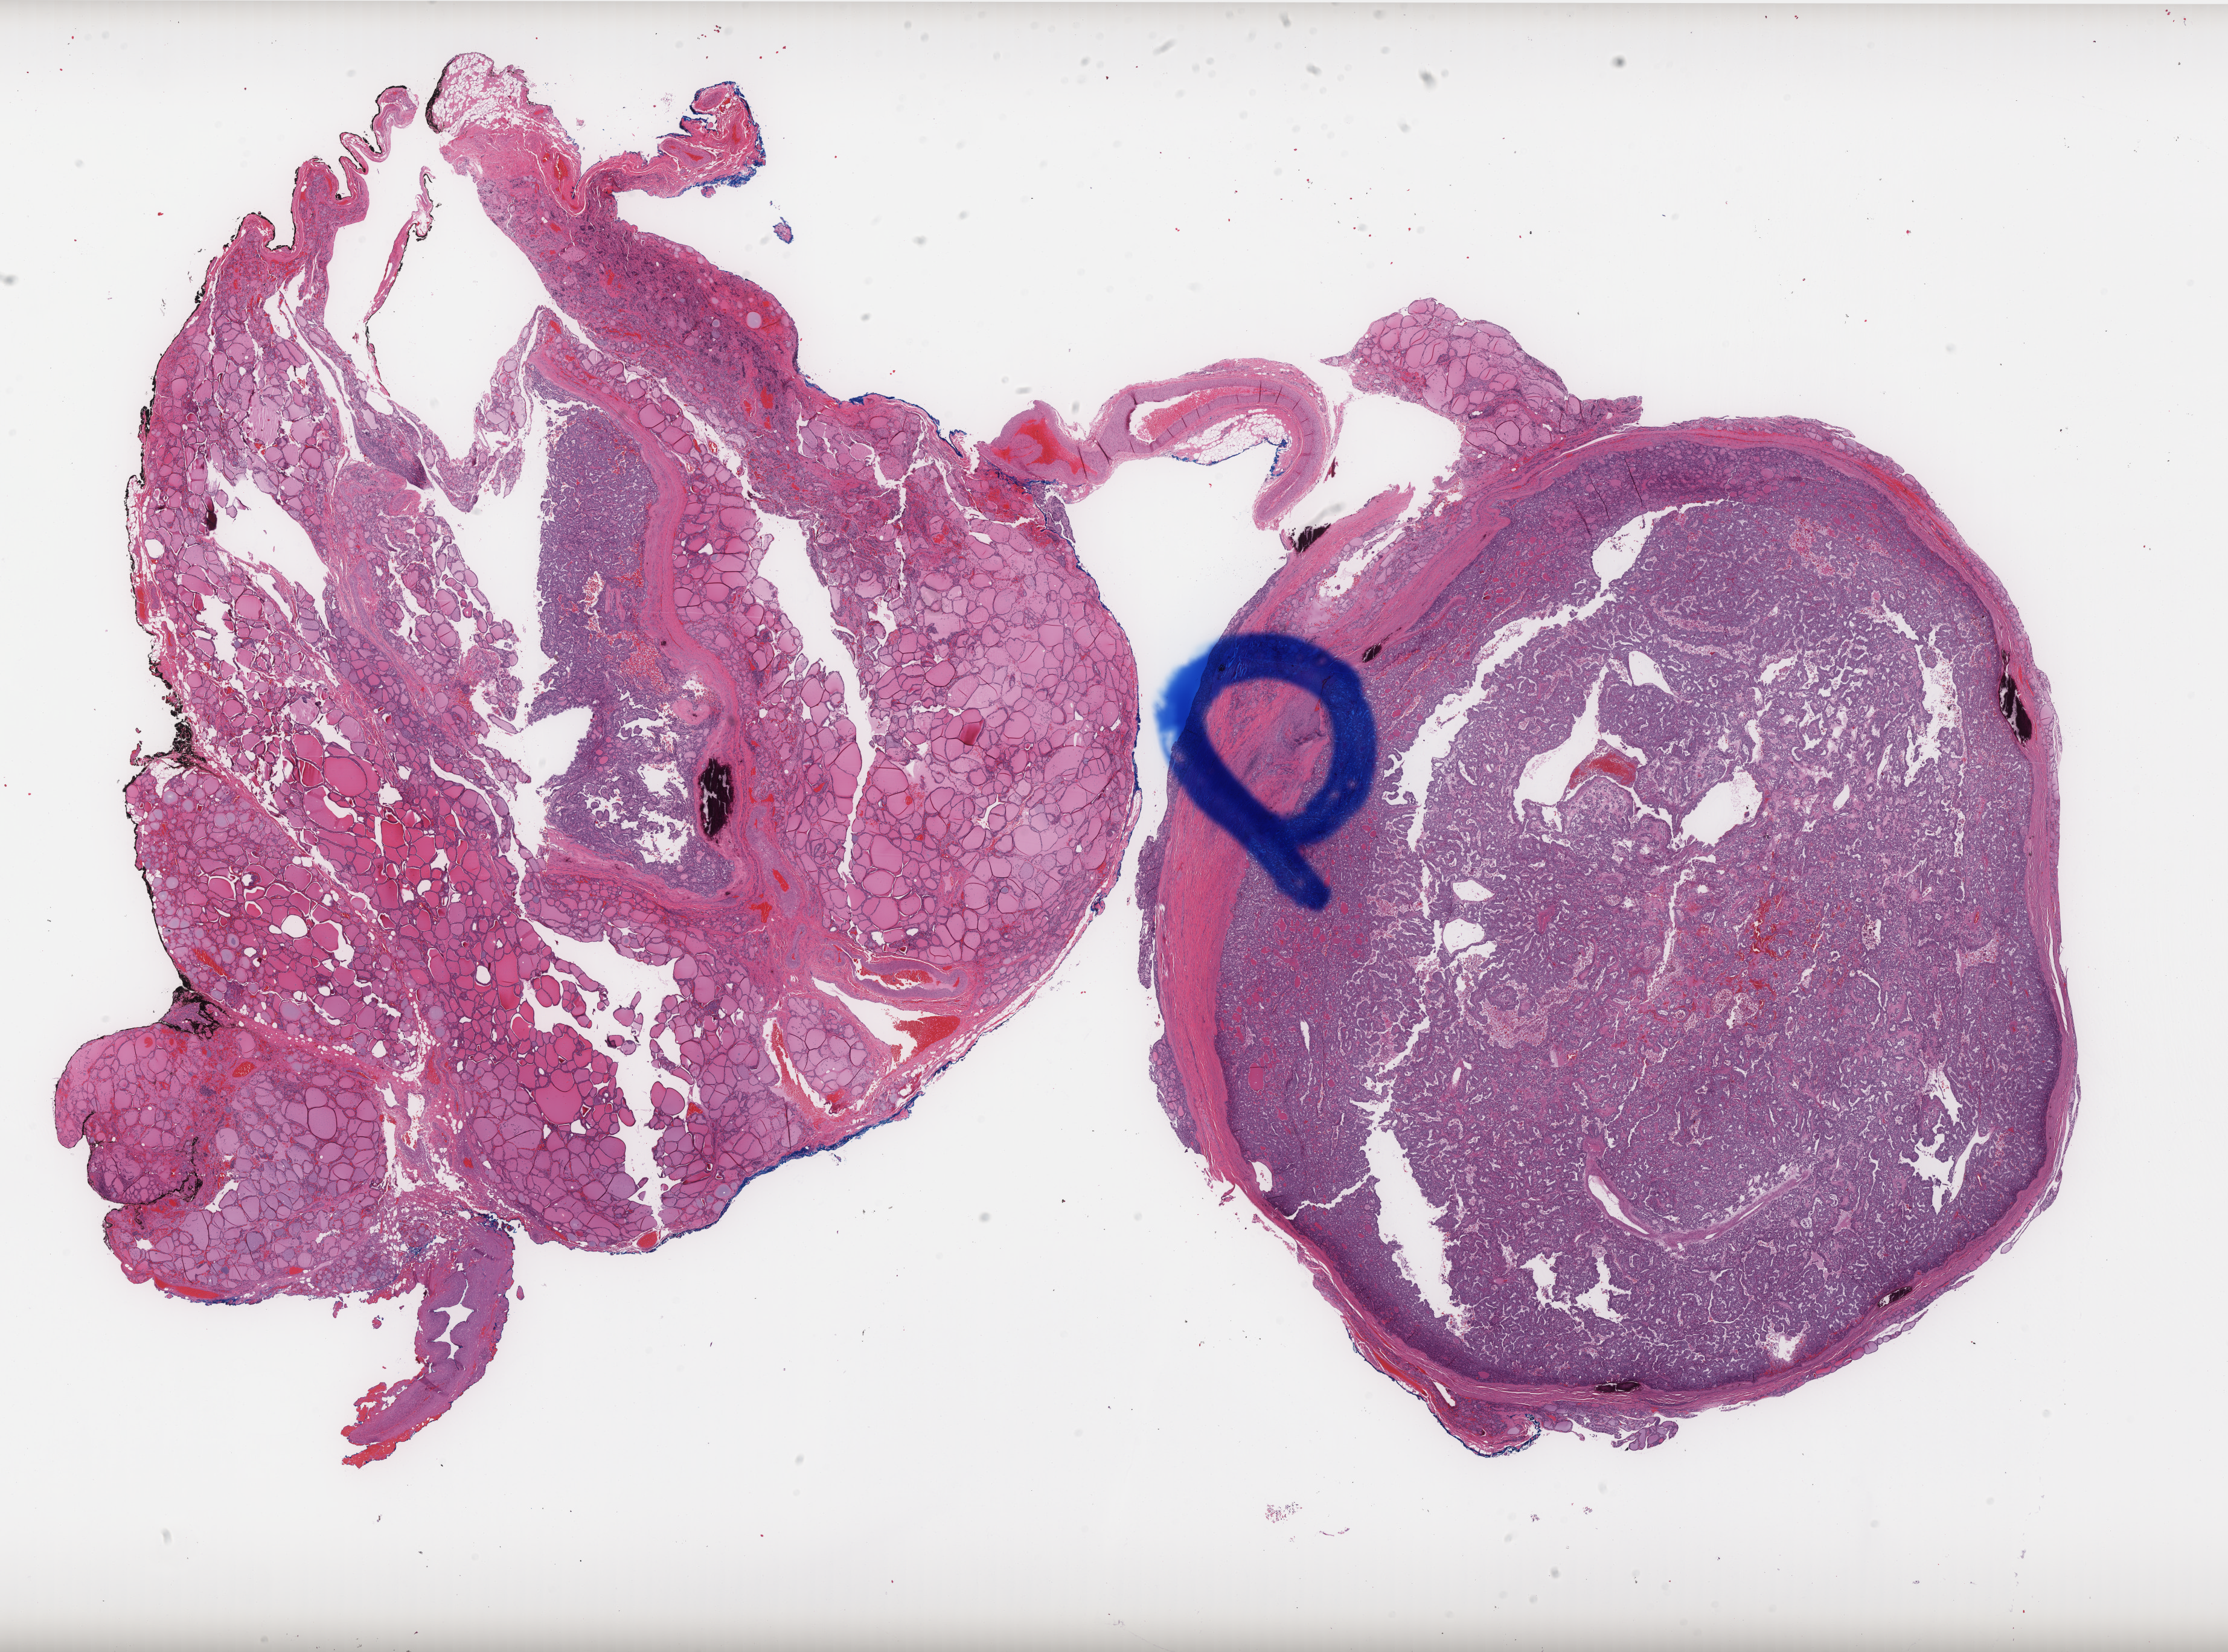
H&E-stained whole-slide image, whole scanned area (about 29.6 x 21.9 mm, slide scanned at 40x) shown as a low-resolution overview; formalin-fixed paraffin-embedded (FFPE) diagnostic section; thyroid, primary tumour sample. Female, age 42 years at initial diagnosis.
Histologic diagnosis: Papillary adenocarcinoma, NOS (thyroid gland). TNM: T1b N0 M0. AJCC pathologic stage: I.